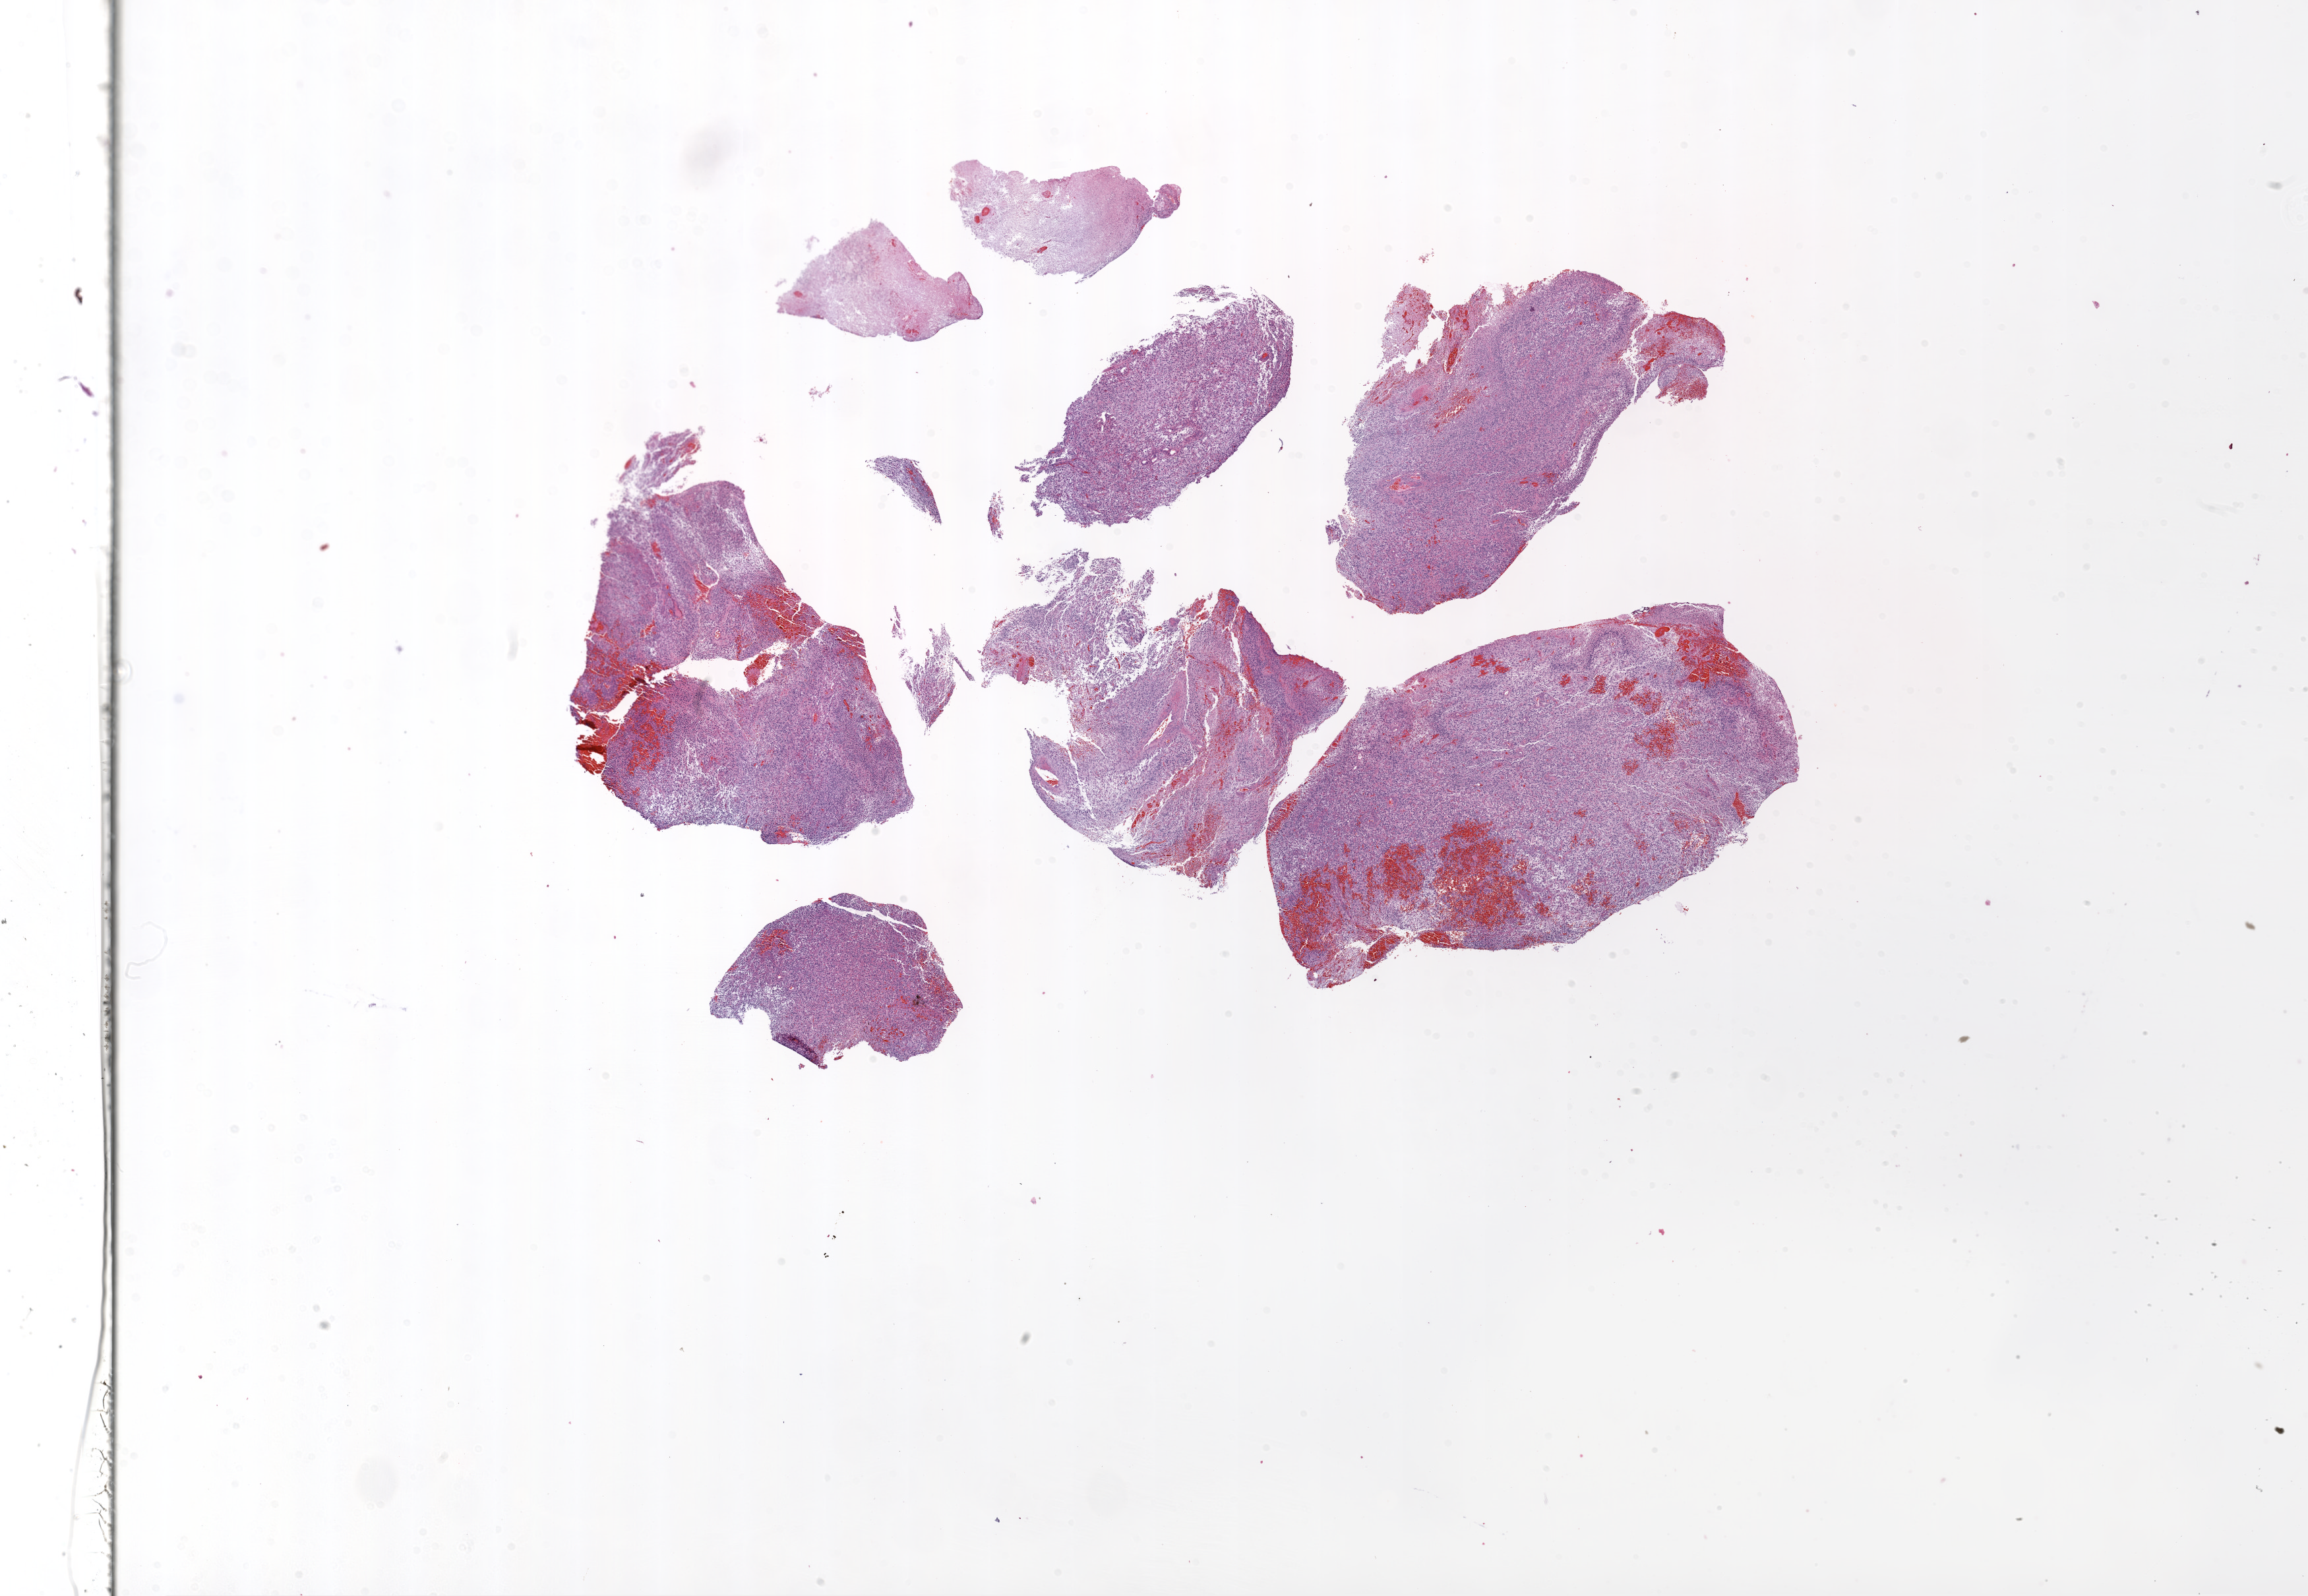
Hematoxylin and eosin (H&E) stained whole-slide image, whole scanned area (about 28.1 x 19.4 mm, slide scanned at 20x) shown as a low-resolution overview; FFPE section; sample: primary tumour, brain. Patient: male, age at initial diagnosis 59 years.
- diagnosis: Glioblastoma